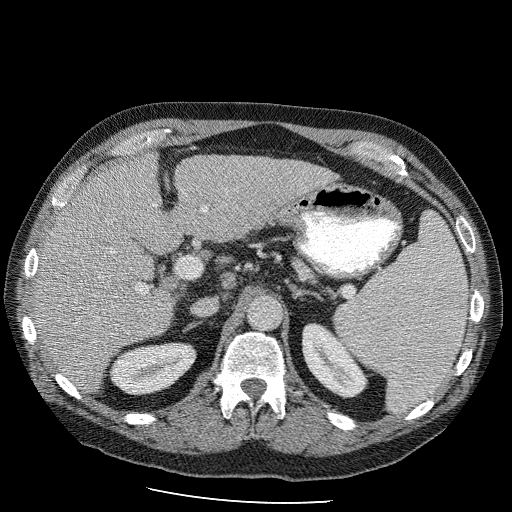
Contrast-enhanced abdominal CT (liver protocol), one axial slice; position 58 of 98 along the scan axis; reconstruction kernel STANDARD; 120 kVp; soft-tissue window (W 400 / L 40 HU); 512 × 512 image matrix, field of view 400 × 400 mm. From the clinical record (not read from this slice): diagnosis: hepatocellular carcinoma (patient treated with transarterial chemoembolisation; whether this scan precedes or follows treatment is not stated here); TNM stage (as recorded): Stage-II; Child-Pugh class: B.
Outlined on this slice (semi-automatically segmented with operator editing):
- liver parenchyma outside the tumour (the mass and vessels are separate outlines, so this box may not span the whole liver): box from (x=34, y=150) to (x=348, y=394) px